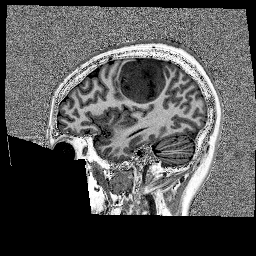
Brain MRI from a brain-tumour surgery series, one sagittal slice; slice 51 of 176 in the series (ordered by position); 1 mm slice thickness; 256 × 256 image matrix, field of view 256 × 256 mm. From the clinical record (not read from this slice): histopathology: Glioblastoma; WHO grade: 4; IDH mutation: no; tumour location: Left Frontal.
Structures marked on this image (manually delineated by an expert):
- tumour: bounding box (x1, y1, x2, y2) in pixels: (118, 58, 175, 105)